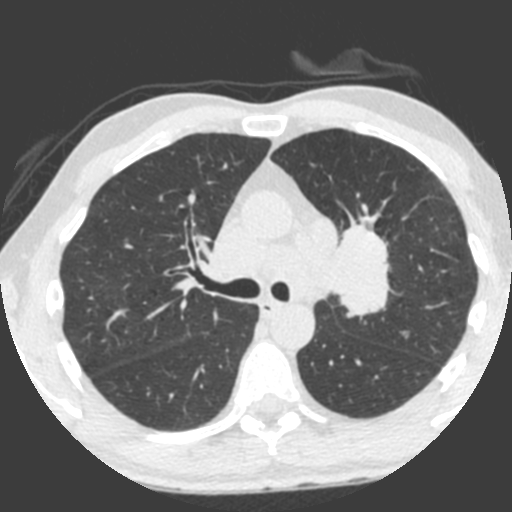
Low-dose screening chest CT, axial slice. Third annual screen. Lung window (W 1500 / L -600 HU). 2 mm slice thickness. Standard (soft-tissue) reconstruction kernel (B). Slice 142 of 212 in the series. 512 × 512 image matrix, field of view 315 × 315 mm. Male, age 55 years at enrolment.
Expert reader's lesion annotation, bounding box [x1, y1, x2, y2] px = [309, 224, 394, 324]. Reader record for this screening exam (exam-level; its link to the box is not recorded): non-calcified nodule or mass ≥4 mm, left upper lobe, 49 × 29 mm, spiculated (stellate) margins, soft tissue attenuation, pre-existing on the prior screen: yes; interval growth: yes. Lung cancer was diagnosed 0 days after this screen: small cell carcinoma, NOS, left upper lobe, undifferentiated (G4), stage IV (AJCC 6th edition), 60 mm at pathology.